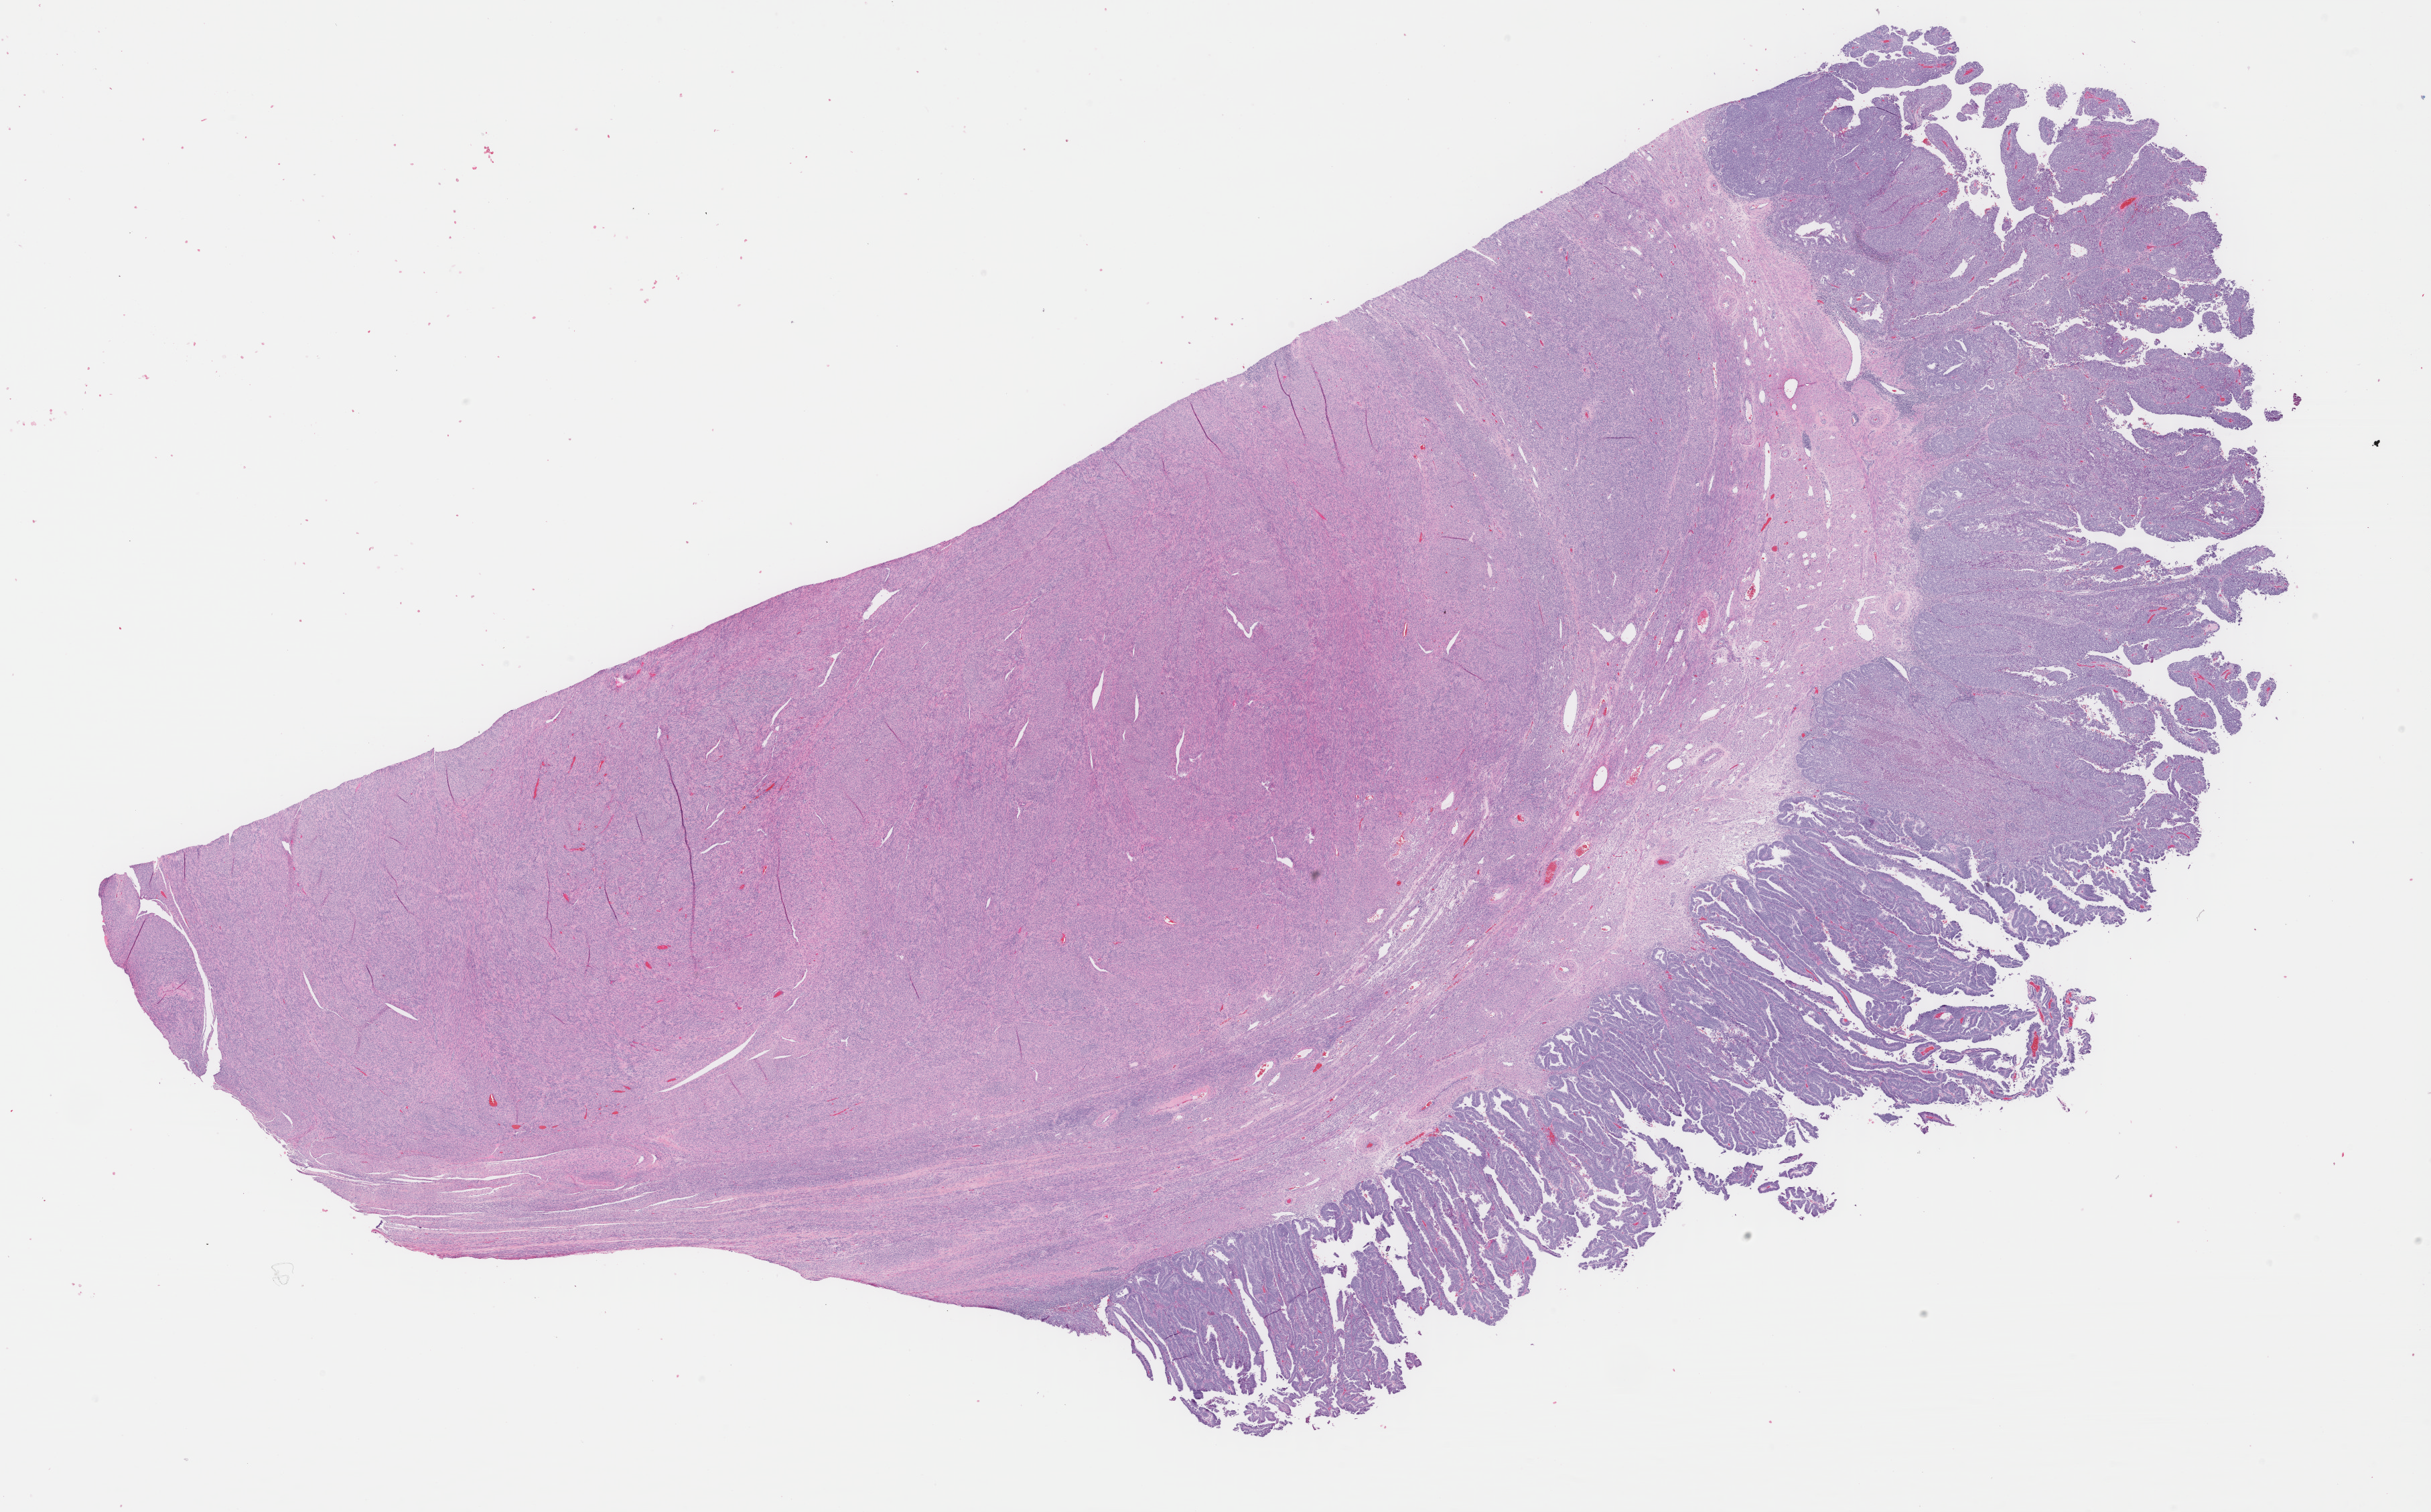
Digitized H&E-stained tissue section (whole slide) — low-resolution overview of the scanned area, about 28.8 x 17.9 mm (acquisition: 40x scan), FFPE section, sample: primary tumour, uterus. Female patient; age at initial diagnosis 62 years. Histologic grade: G3 (poorly differentiated).
FIGO stage: IA. Diagnosis: Endometrioid adenocarcinoma, NOS (endometrium).